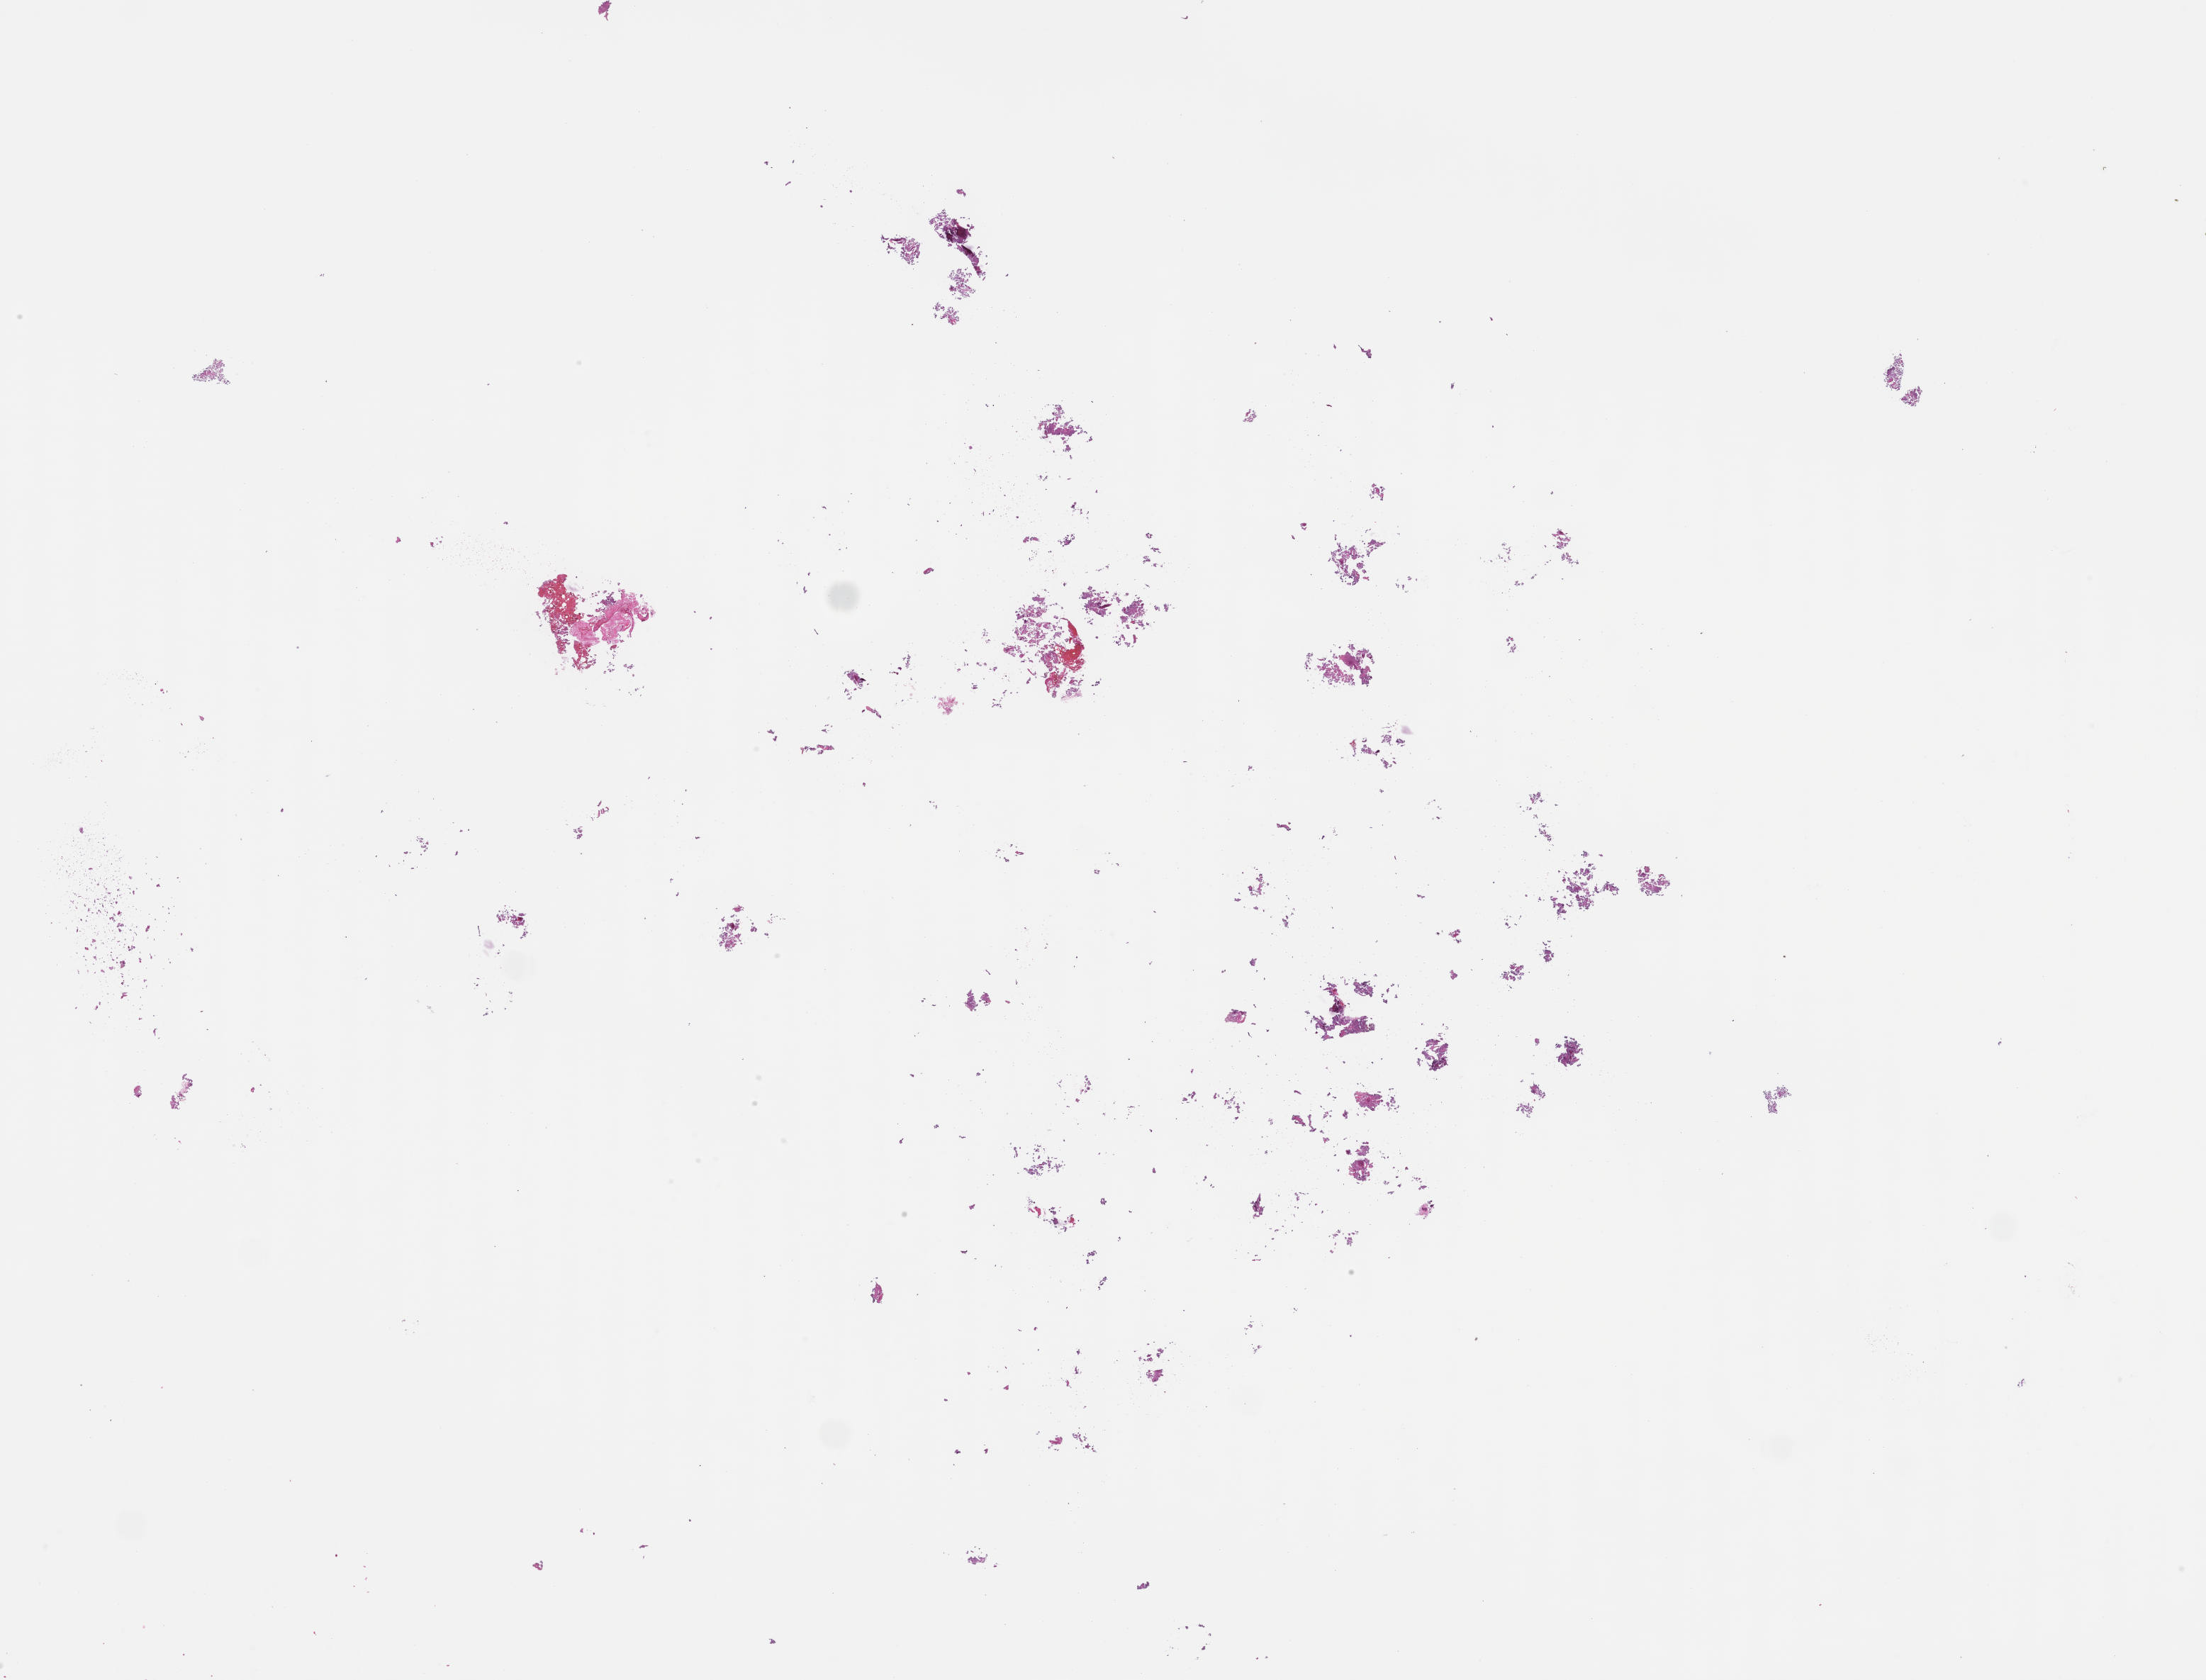
H&E whole-slide image, a low-resolution overview of the entire scanned area, about 25.1 x 19.1 mm. FFPE section. Specimen time point: collected at disease progression. Patient sex: male.
- this section: metastasis (sampled organ not recorded)
- patient diagnosis (primary): Prostate Carcinoma